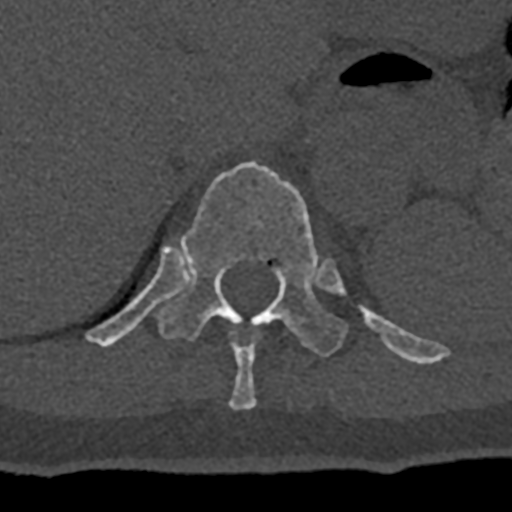
CT including the spine, one axial slice. Slice 560 of 797 in the series (ordered by position). Reconstruction kernel Br40s/3. Bone window (W 1800 / L 400 HU). 0.5 mm slice thickness. 512 × 512 image matrix, field of view 160 × 160 mm. Male patient, age 74 years. Case-level facts recorded for this patient, not image findings: primary cancer: renal; vertebrae with lytic lesions (as recorded): T10, L1, L2, L3, L4, L5.
Annotated regions visible in this slice (semi-automatic segmentation, software-assisted and operator-edited):
- T10 vertebra: bounding box [x1, y1, x2, y2] px = [229, 330, 261, 409]
- T11 vertebra: [86, 162, 432, 364]